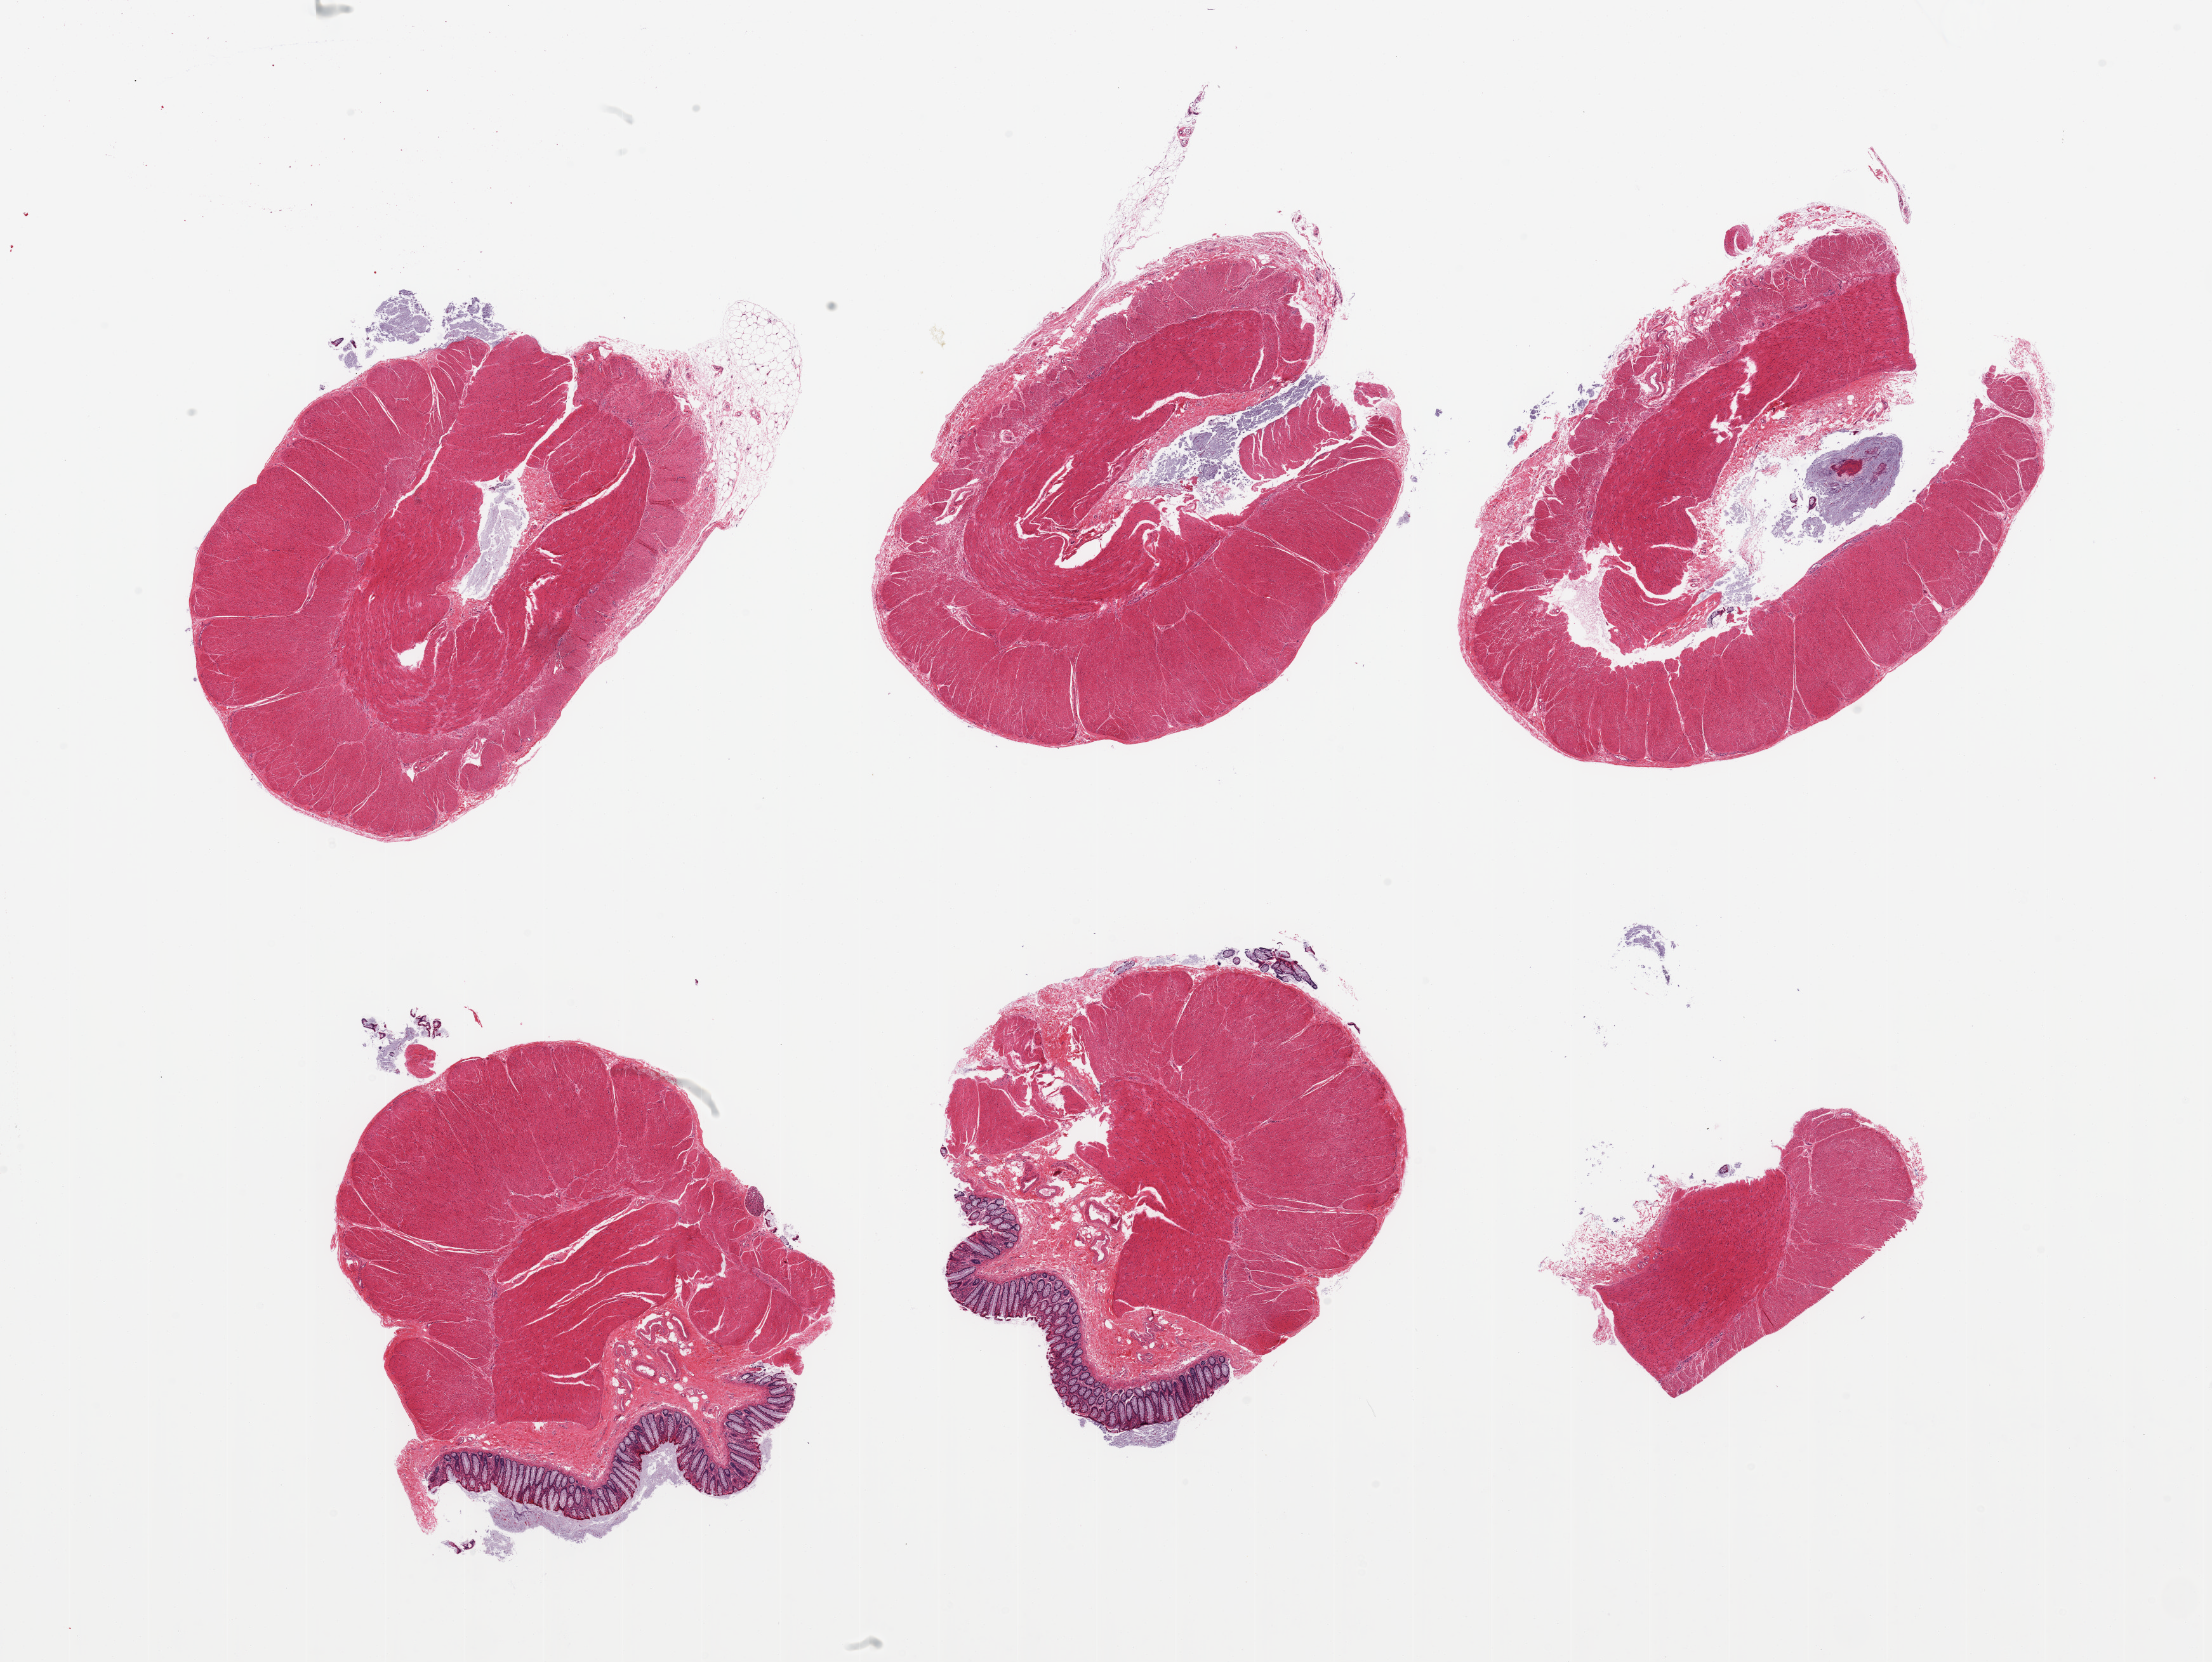
Whole-slide image, haematoxylin and eosin stain, whole scanned area (about 27.6 x 20.7 mm, from a 20x scan) shown as a low-resolution overview; PAXgene-fixed paraffin-embedded (PFPE) section; sampled site (target tissue): sigmoid colon; tissue donor sample. Donor sex: male.
Review note (as recorded): 6 pieces; 2 contain mucosa as well as muscularis.